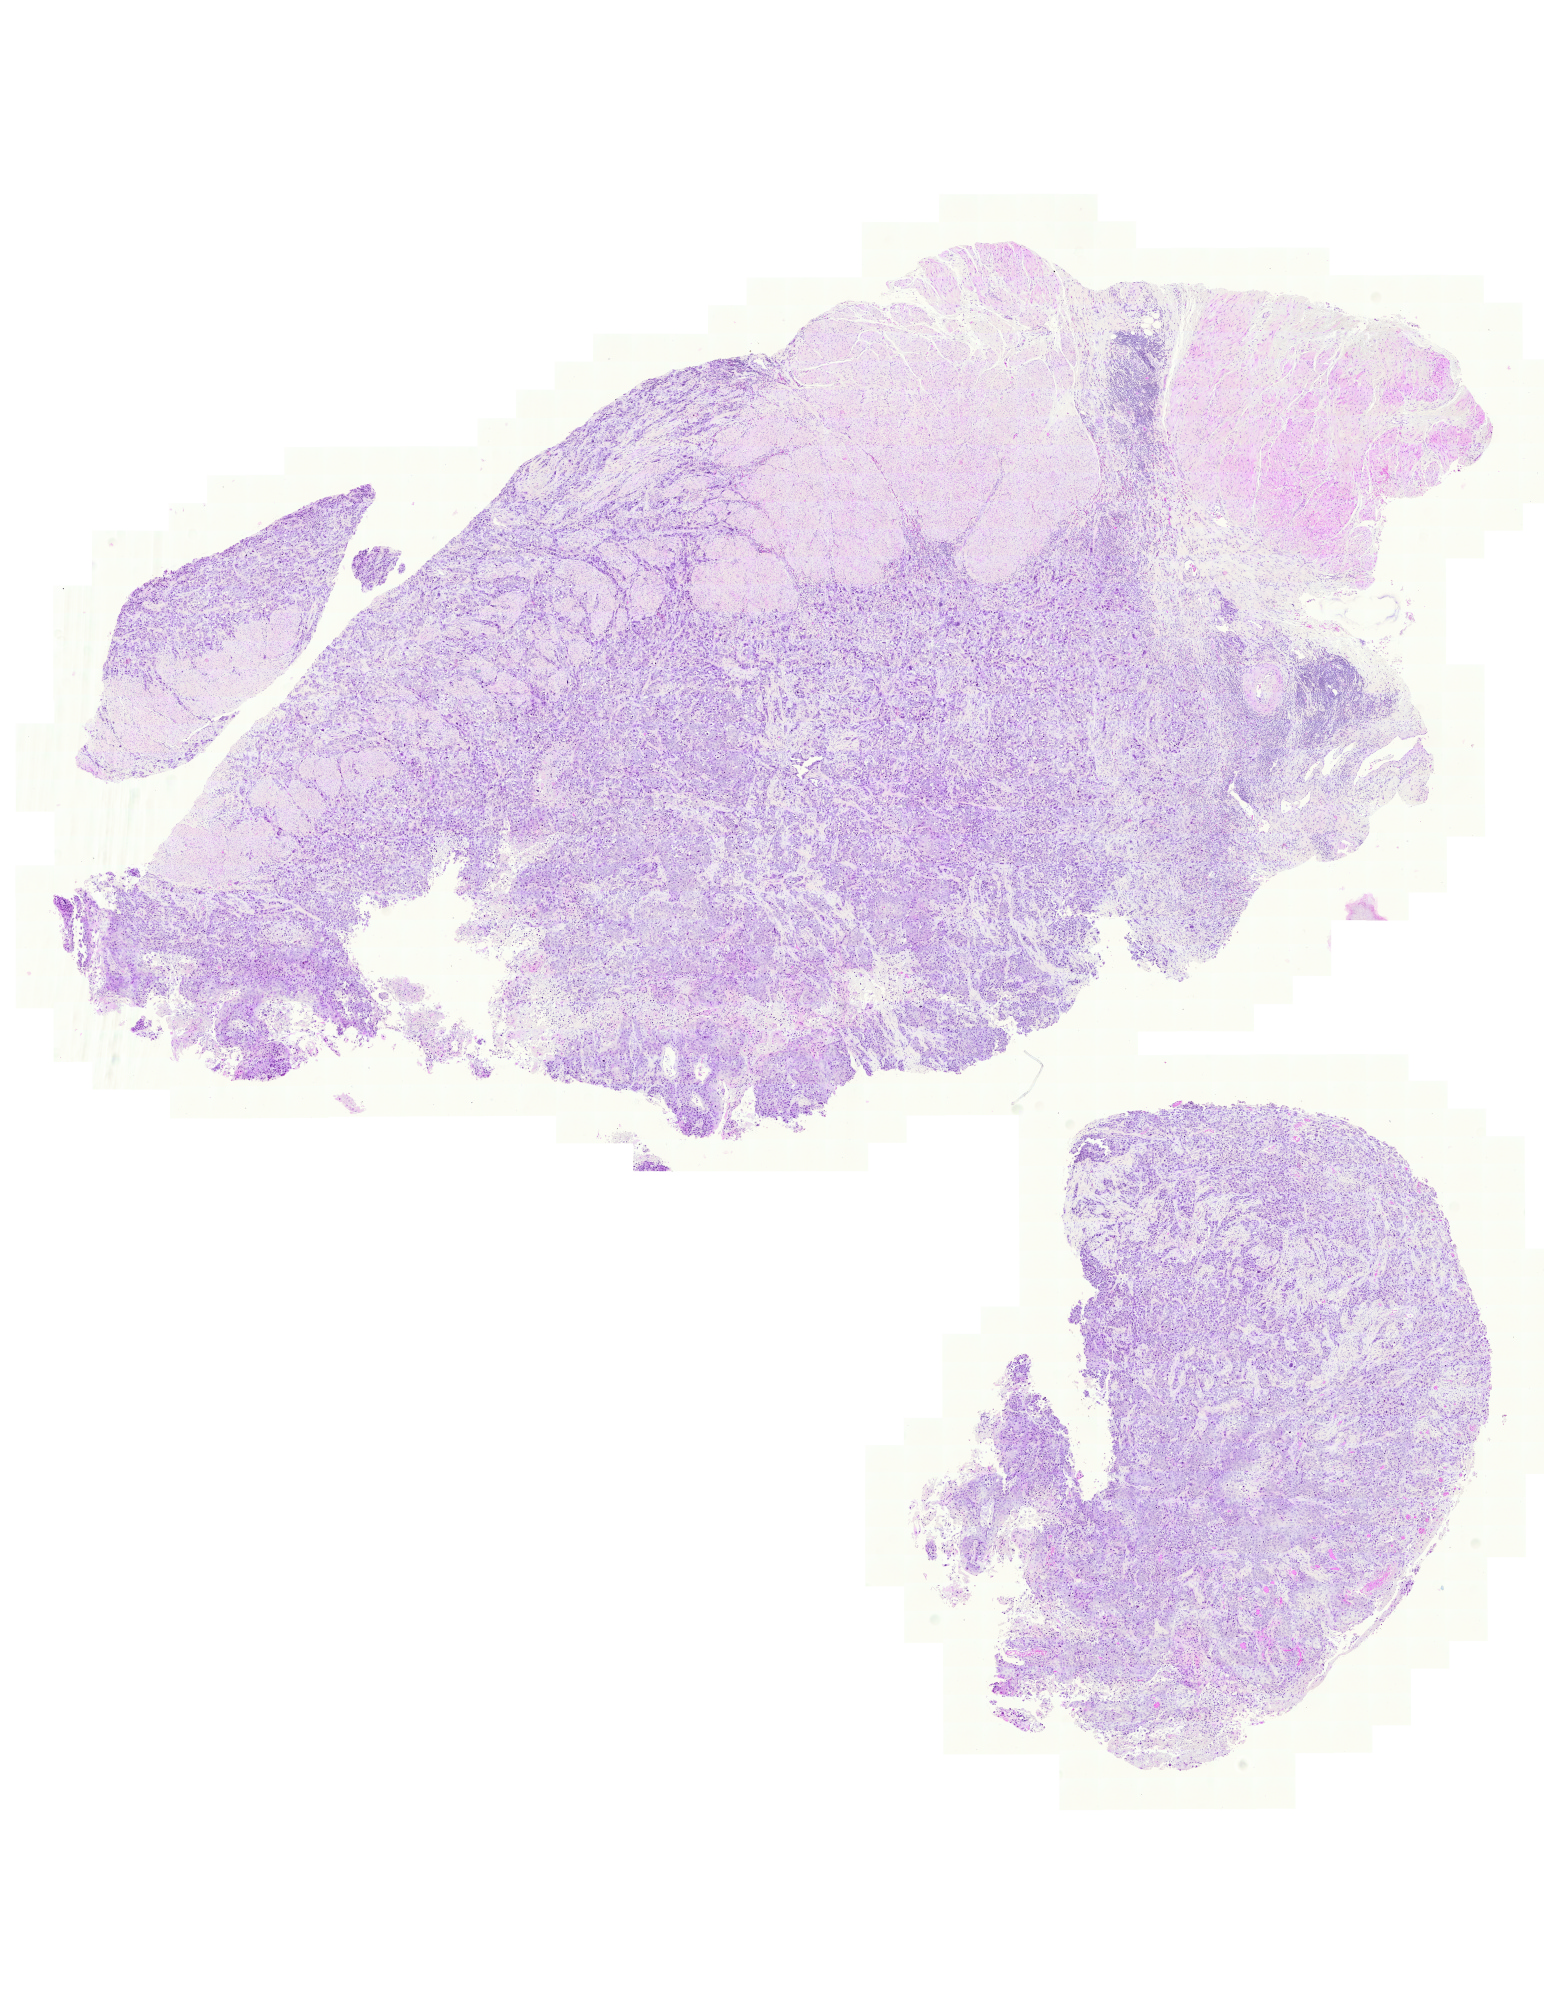
Digitized Hematoxylin and eosin (H&E) stained tissue section (whole slide), a low-resolution overview of the entire scanned area, about 11.5 x 14.8 mm (from a 20x scan); formalin-fixed paraffin-embedded (FFPE) diagnostic section; primary tumour sample from the bladder. Male patient; age at initial diagnosis 60 years. Histologic grade: high grade.
TNM: T2b N0 M0. Diagnosis: Transitional cell carcinoma. AJCC pathologic stage: II (5th edition).